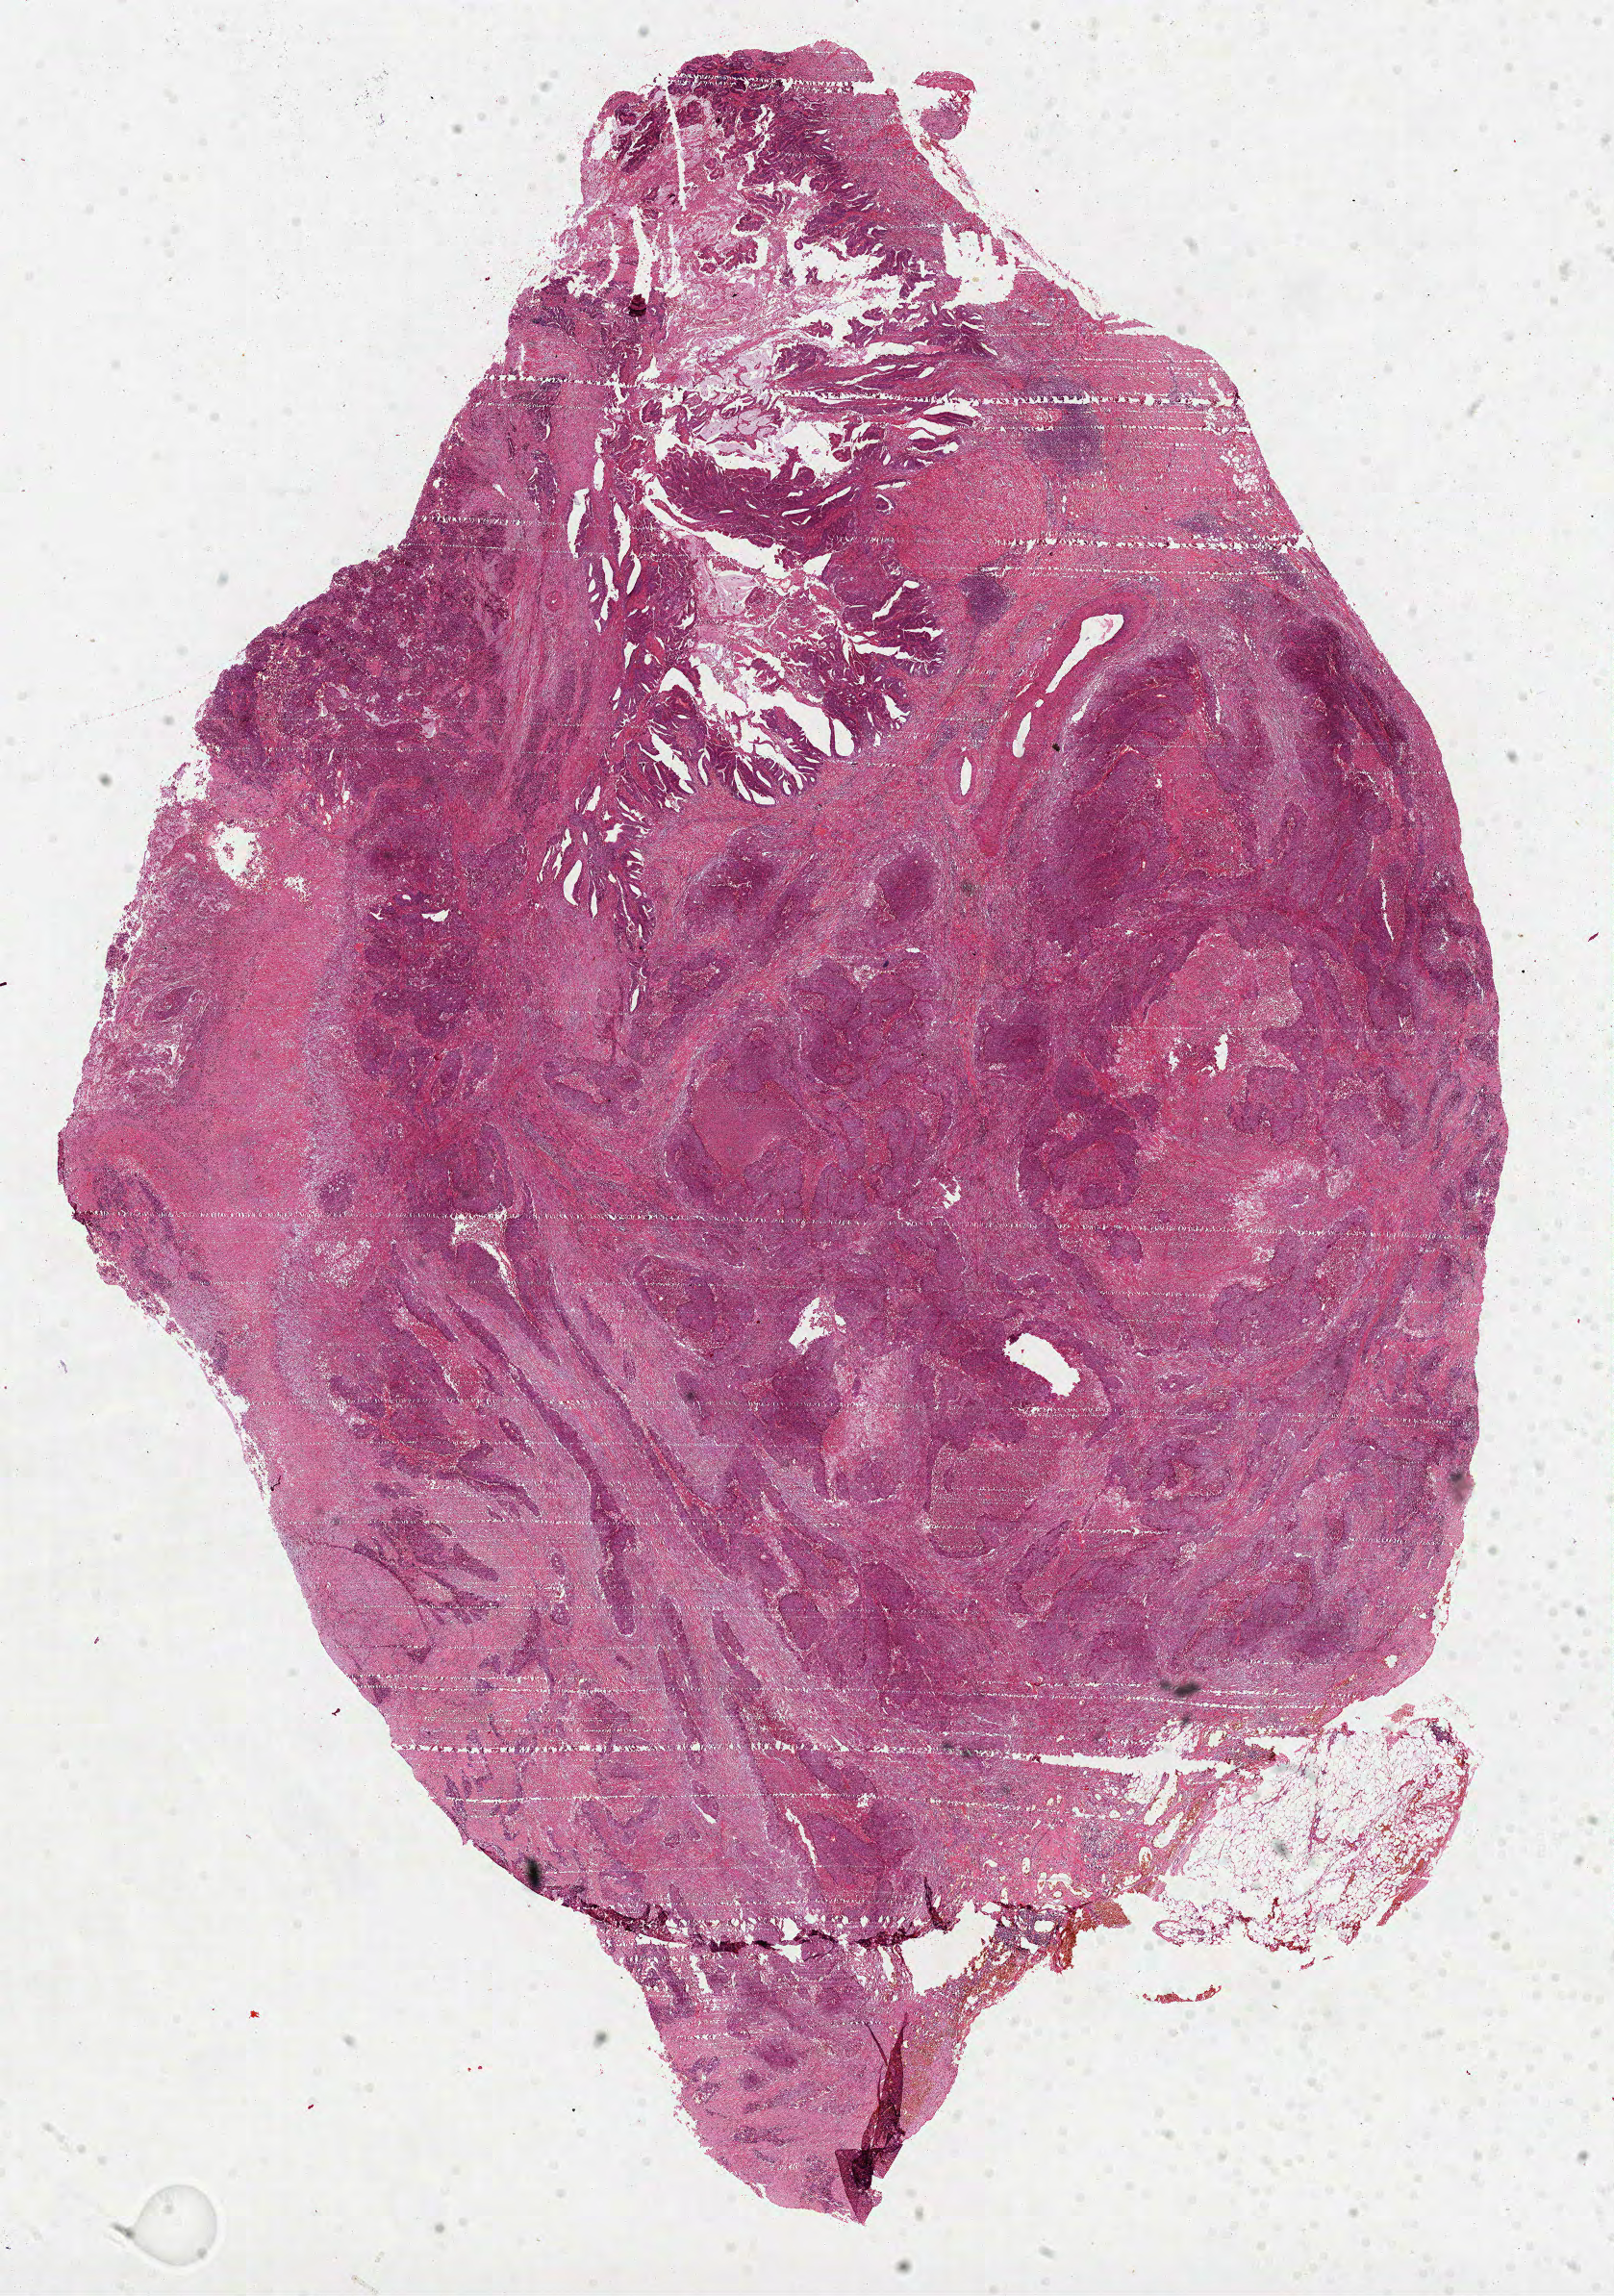
H&E-stained whole-slide image — a low-resolution overview of the entire scanned area, about 13.5 x 19.3 mm. Formalin-fixed paraffin-embedded (FFPE) diagnostic section. Colon, primary tumour sample. Male patient; age at initial diagnosis 57 years.
* pathologic diagnosis: Mucinous adenocarcinoma (ascending colon)
* AJCC pathologic stage: IIA (6th edition)